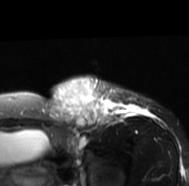
MRI of an extremity soft-tissue mass, one axial slice; slice 56 of 77 in the series (ordered by position); T2-weighted fat-saturated; MR volume resampled by the dataset authors to the PET/CT grid (not the native acquisition matrix); 3.27 mm slice thickness; 189 × 186 image matrix. Female patient. From the clinical record (not read from this slice): histological type: leiomyosarcoma; grade: high; site of the primary tumour: groin.
Annotated regions visible in this slice (expert contour drawn on MRI and transferred to this co-registered scan by the dataset authors):
- gross tumour volume including surrounding oedema: bounding box (x1, y1, x2, y2) in pixels: (49, 75, 153, 131)
- gross tumour volume (mass): (49, 75, 109, 130)